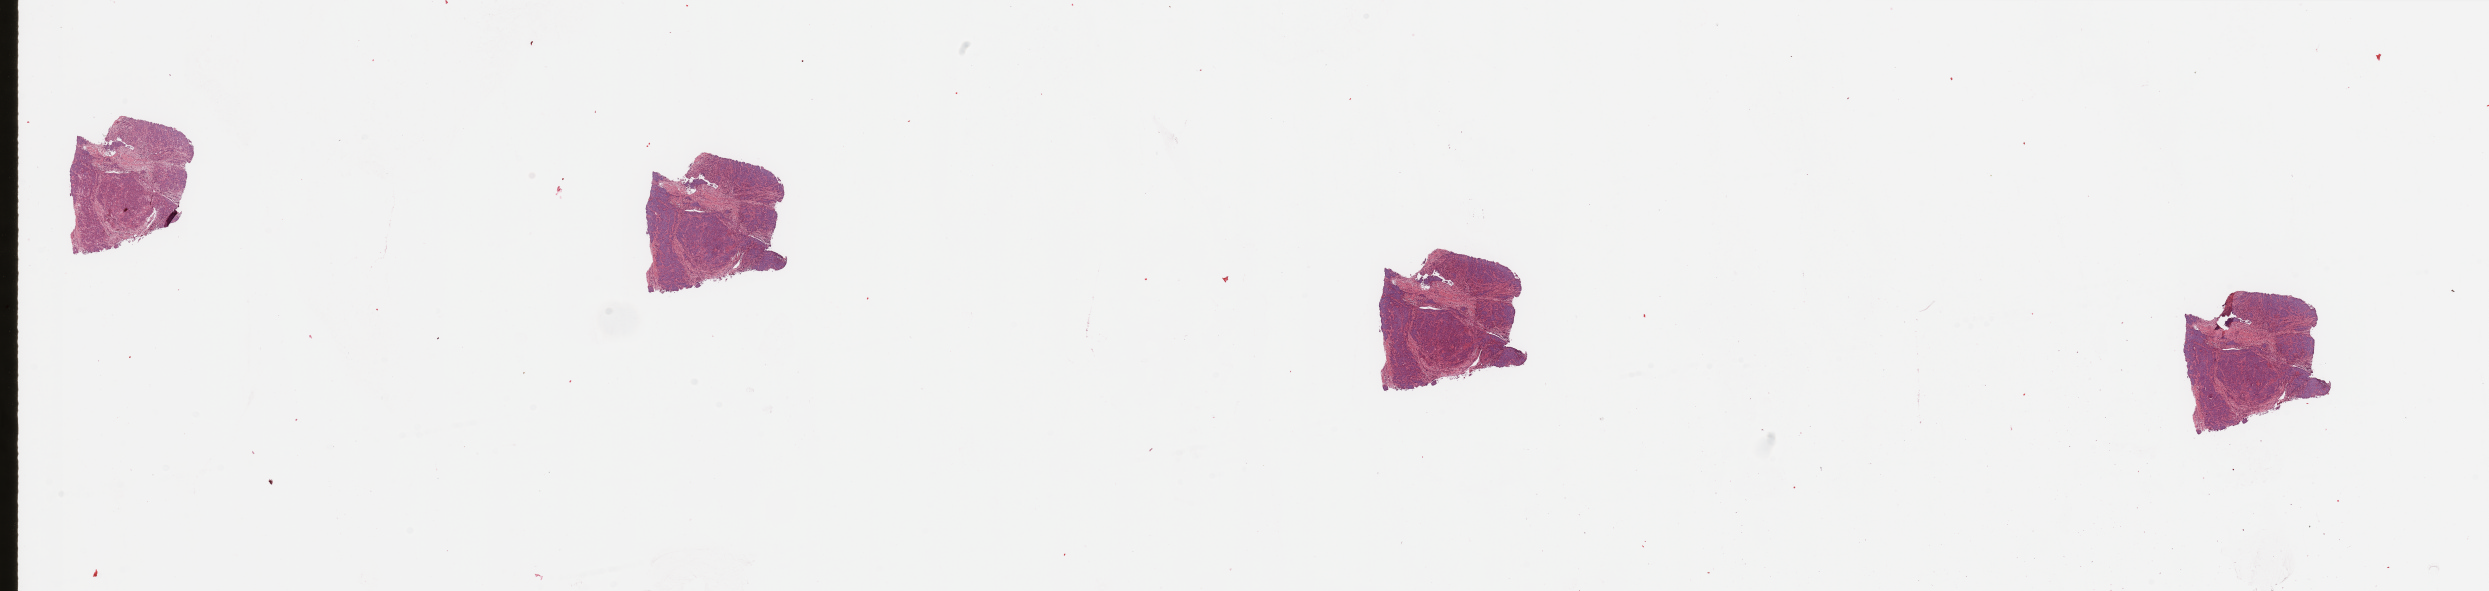
Digitized H&E-stained tissue section (whole slide), a low-resolution overview of the entire scanned area, about 39.4 x 9.3 mm (from a 20x scan). Tumour tissue sample, sampled site: uterus. Patient: female, age 63 years. Histologic grade: G3 (poorly differentiated). Pathologist review of this section (percent, as recorded): tumour nuclei 80%, necrosis 0%.
• AJCC pathologic stage: III
• diagnosis: Endometrioid adenocarcinoma, NOS
• primary tumour site (as recorded): anterior endometrium